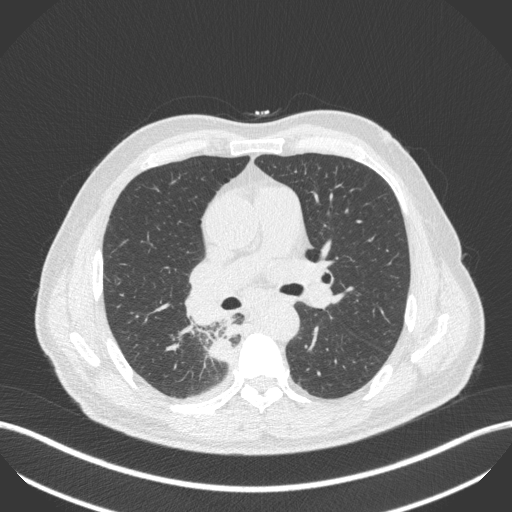
Chest CT, one axial slice; position 272 of 451 along the scan axis; 100 kVp; lung window (W 1500 / L -600 HU); 1 mm slice thickness; 512 × 512 image matrix. Patient: male, 61 years. From the clinical record (not read from this slice): clinical TNM (as recorded): T1 N0 M0.
Structures marked on this image (rectangle marked by the reading radiologist):
- lung tumour (recorded histology: small cell carcinoma): bounding box [x1, y1, x2, y2] px = [207, 333, 238, 364]